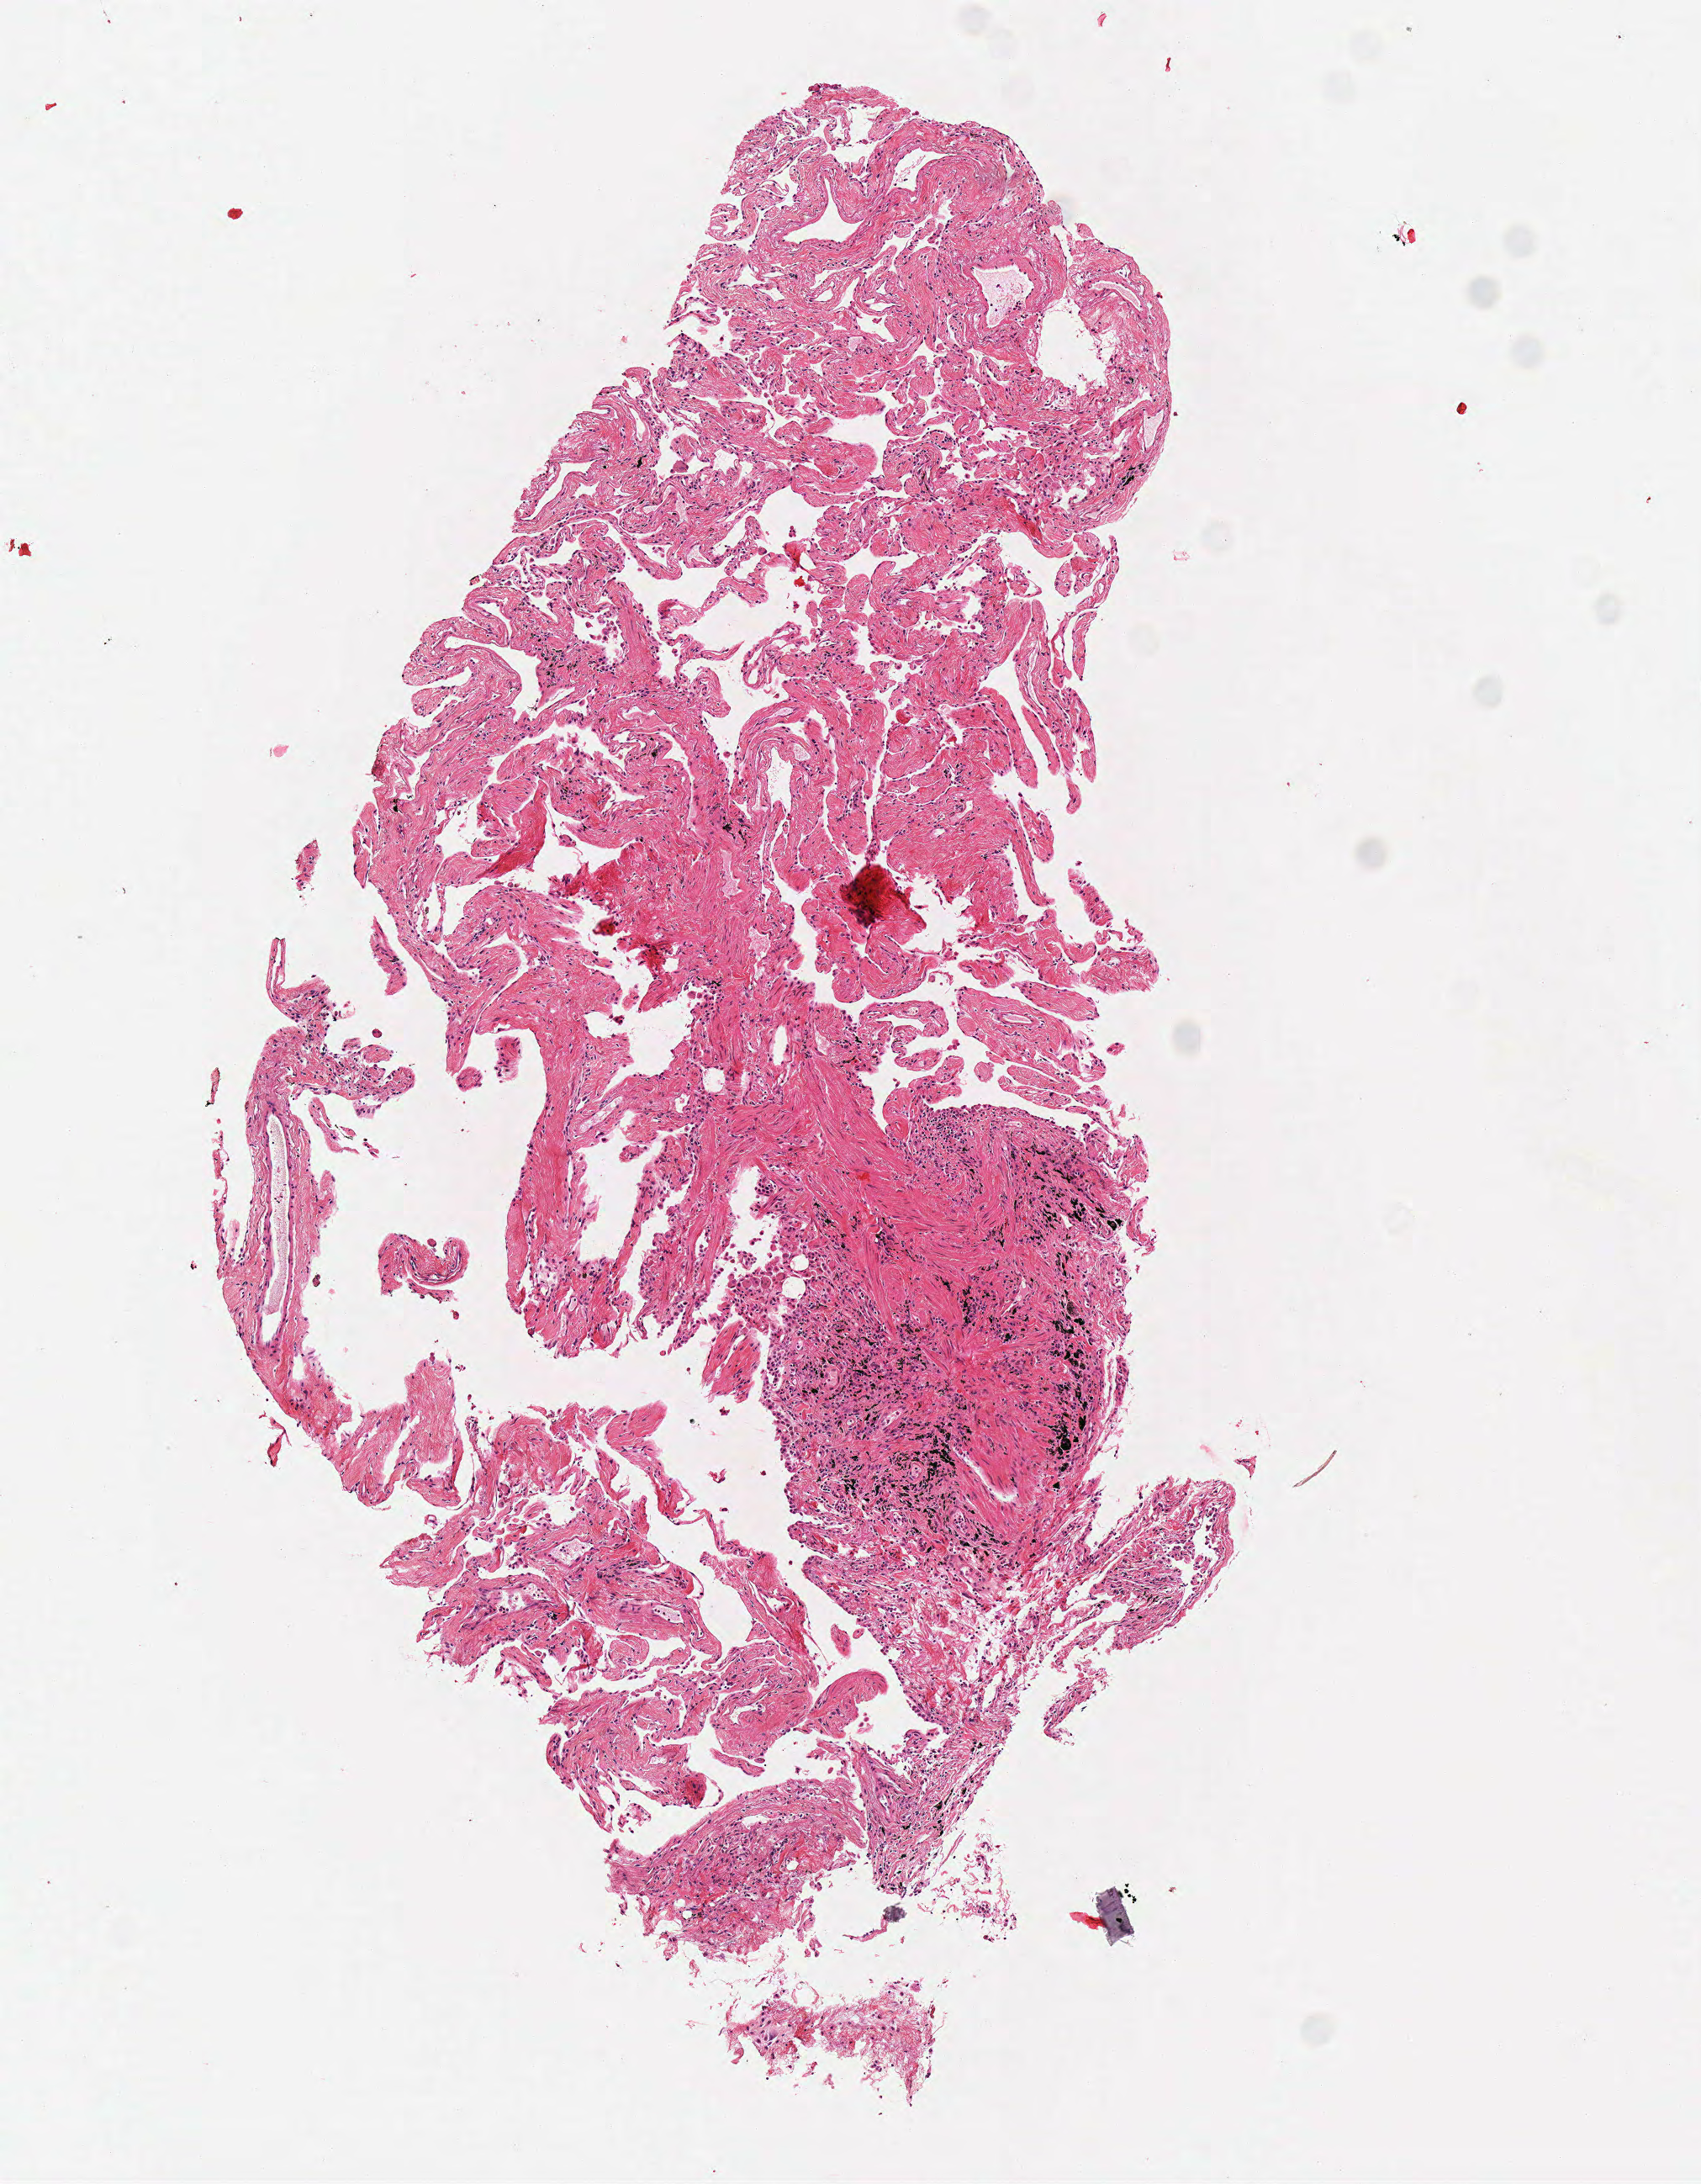
Digitized Hematoxylin and eosin (H&E) stained tissue section (whole slide) — low-resolution overview of the scanned area, about 4.0 x 5.1 mm; frozen section from the top of the tissue portion; solid tissue normal (non-tumour tissue) sample from the lung. Male, age 74 years at initial diagnosis.
* this section: solid tissue normal (non-tumour) sample from the same patient
* patient diagnosis: Squamous cell carcinoma, NOS (lower lobe, lung)